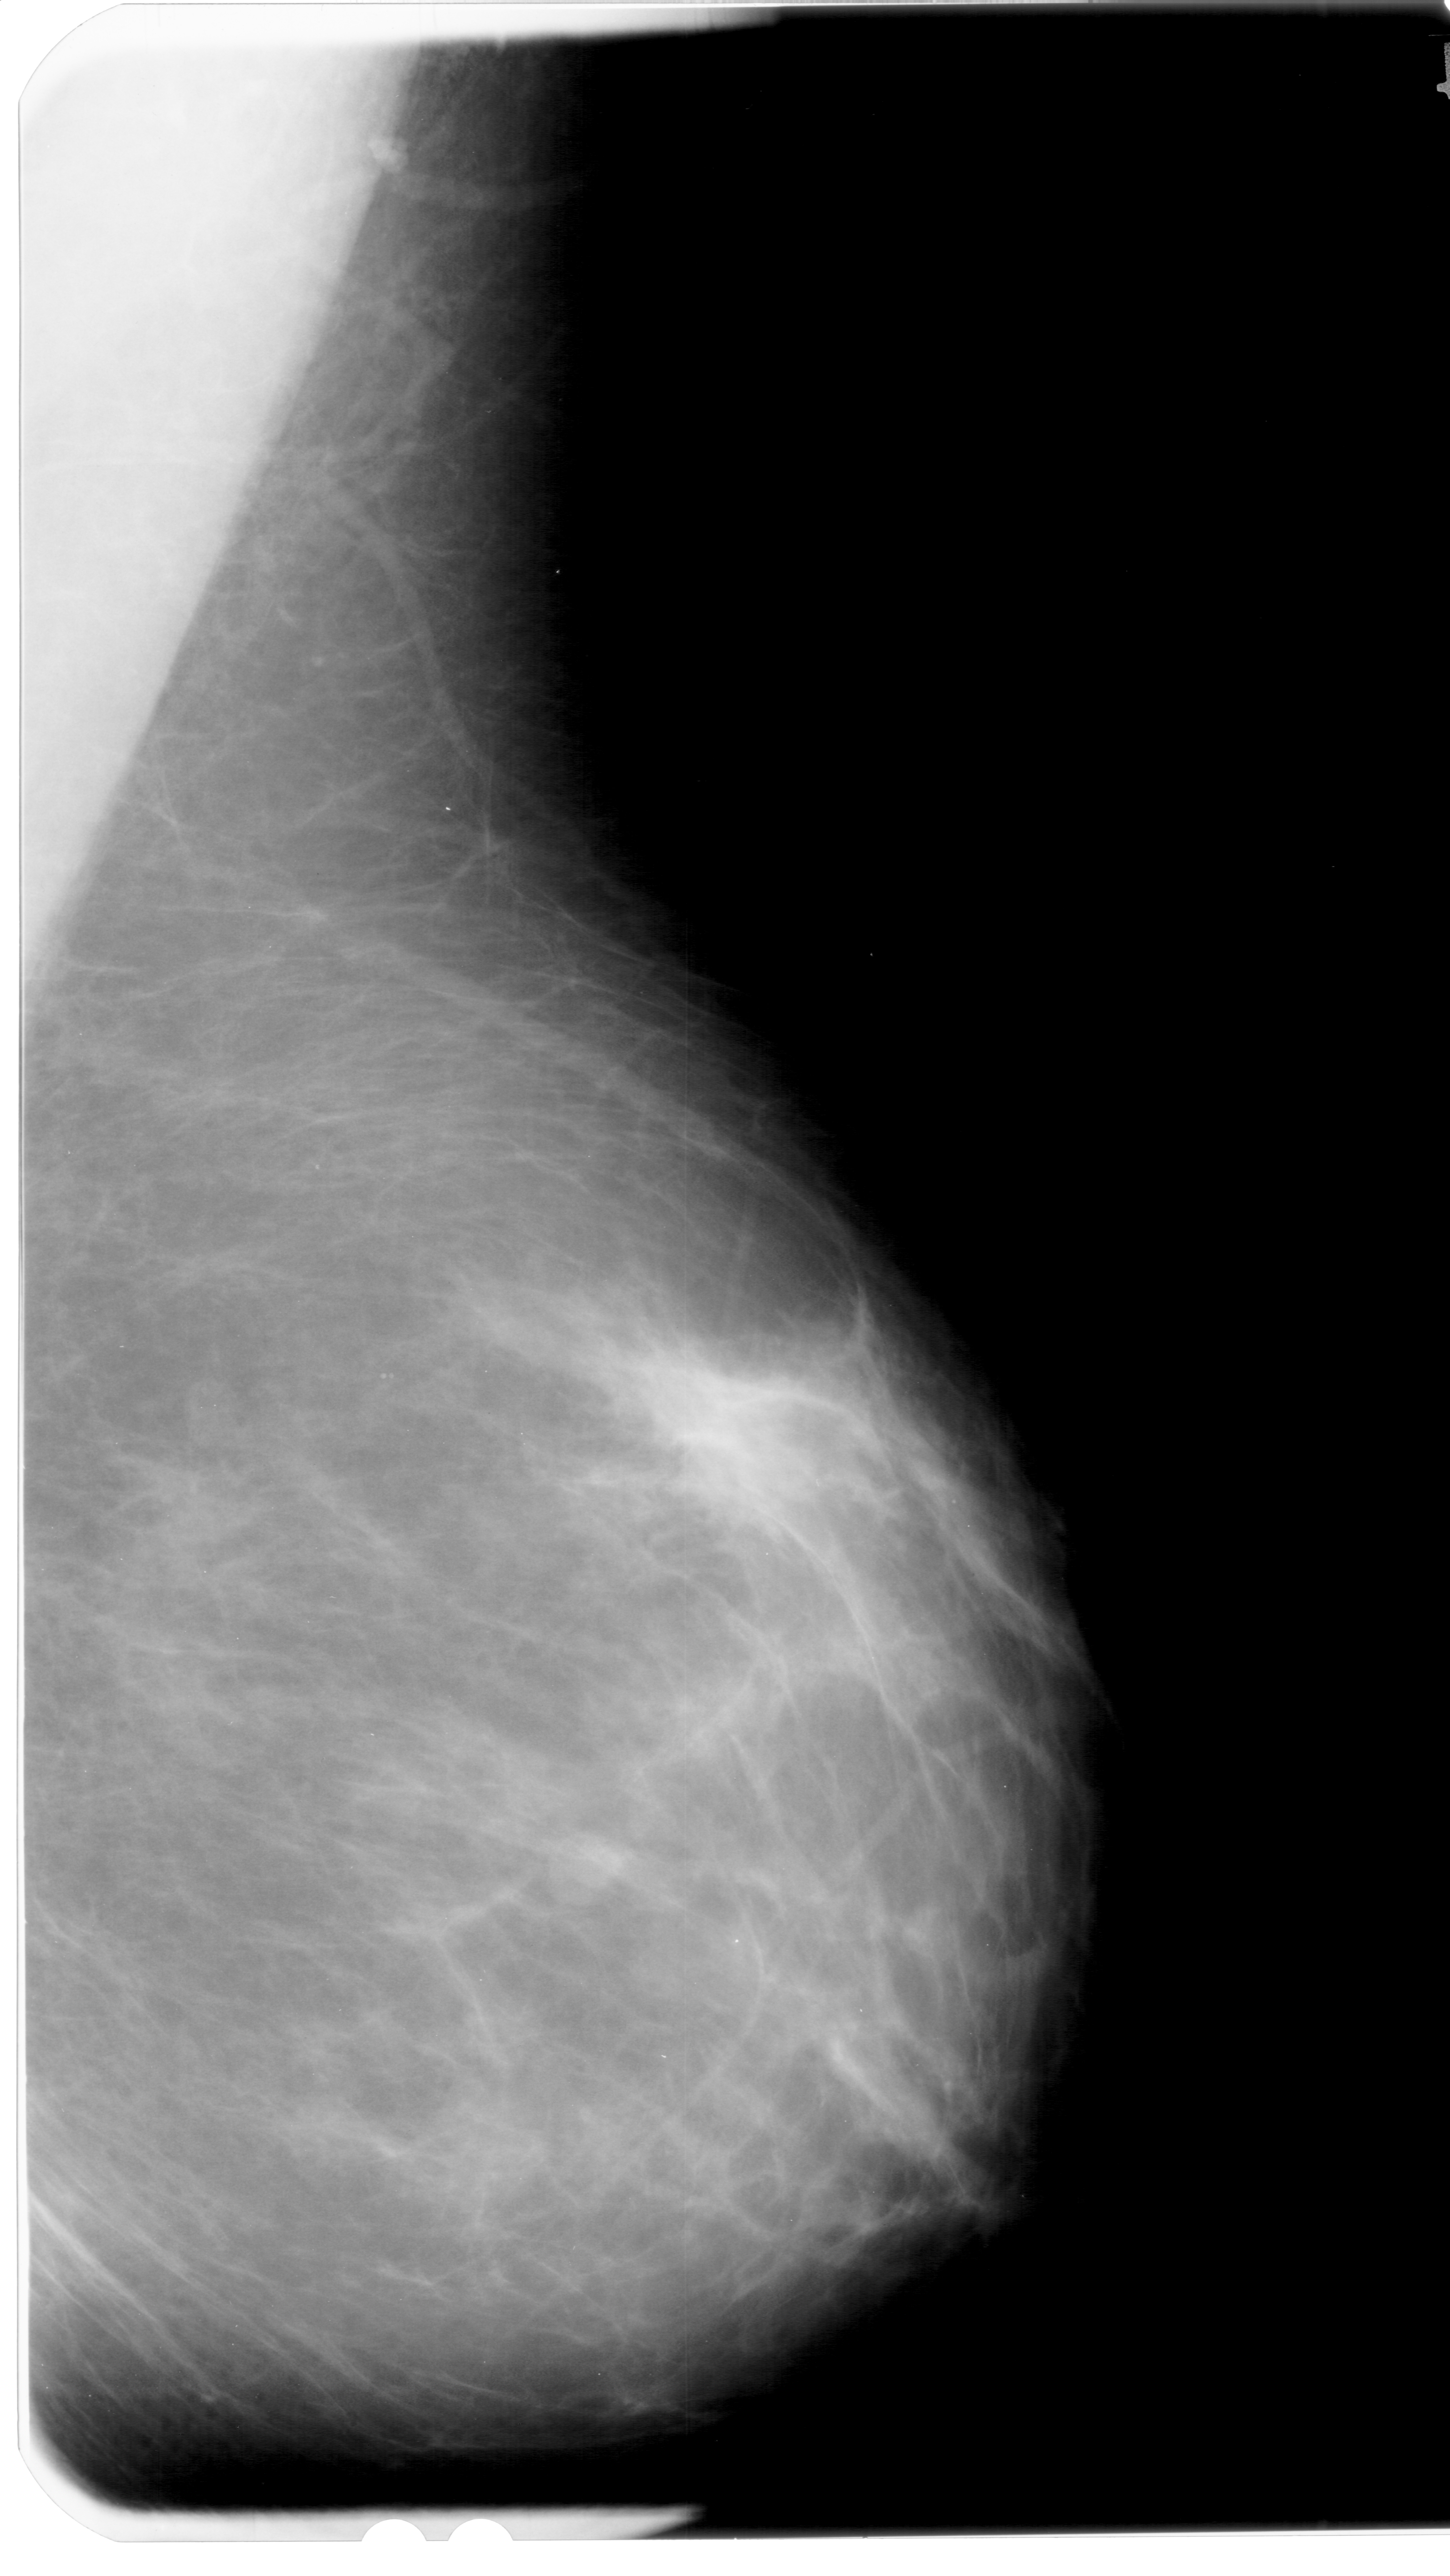
Scanned film-screen mammogram; right breast; mediolateral oblique (MLO) view; breast composition: scattered fibroglandular densities (BI-RADS density category 2 of 4).
Mass, shape round, margins circumscribed; BI-RADS assessment category 3; pathology result (as recorded, not read from the image): benign.